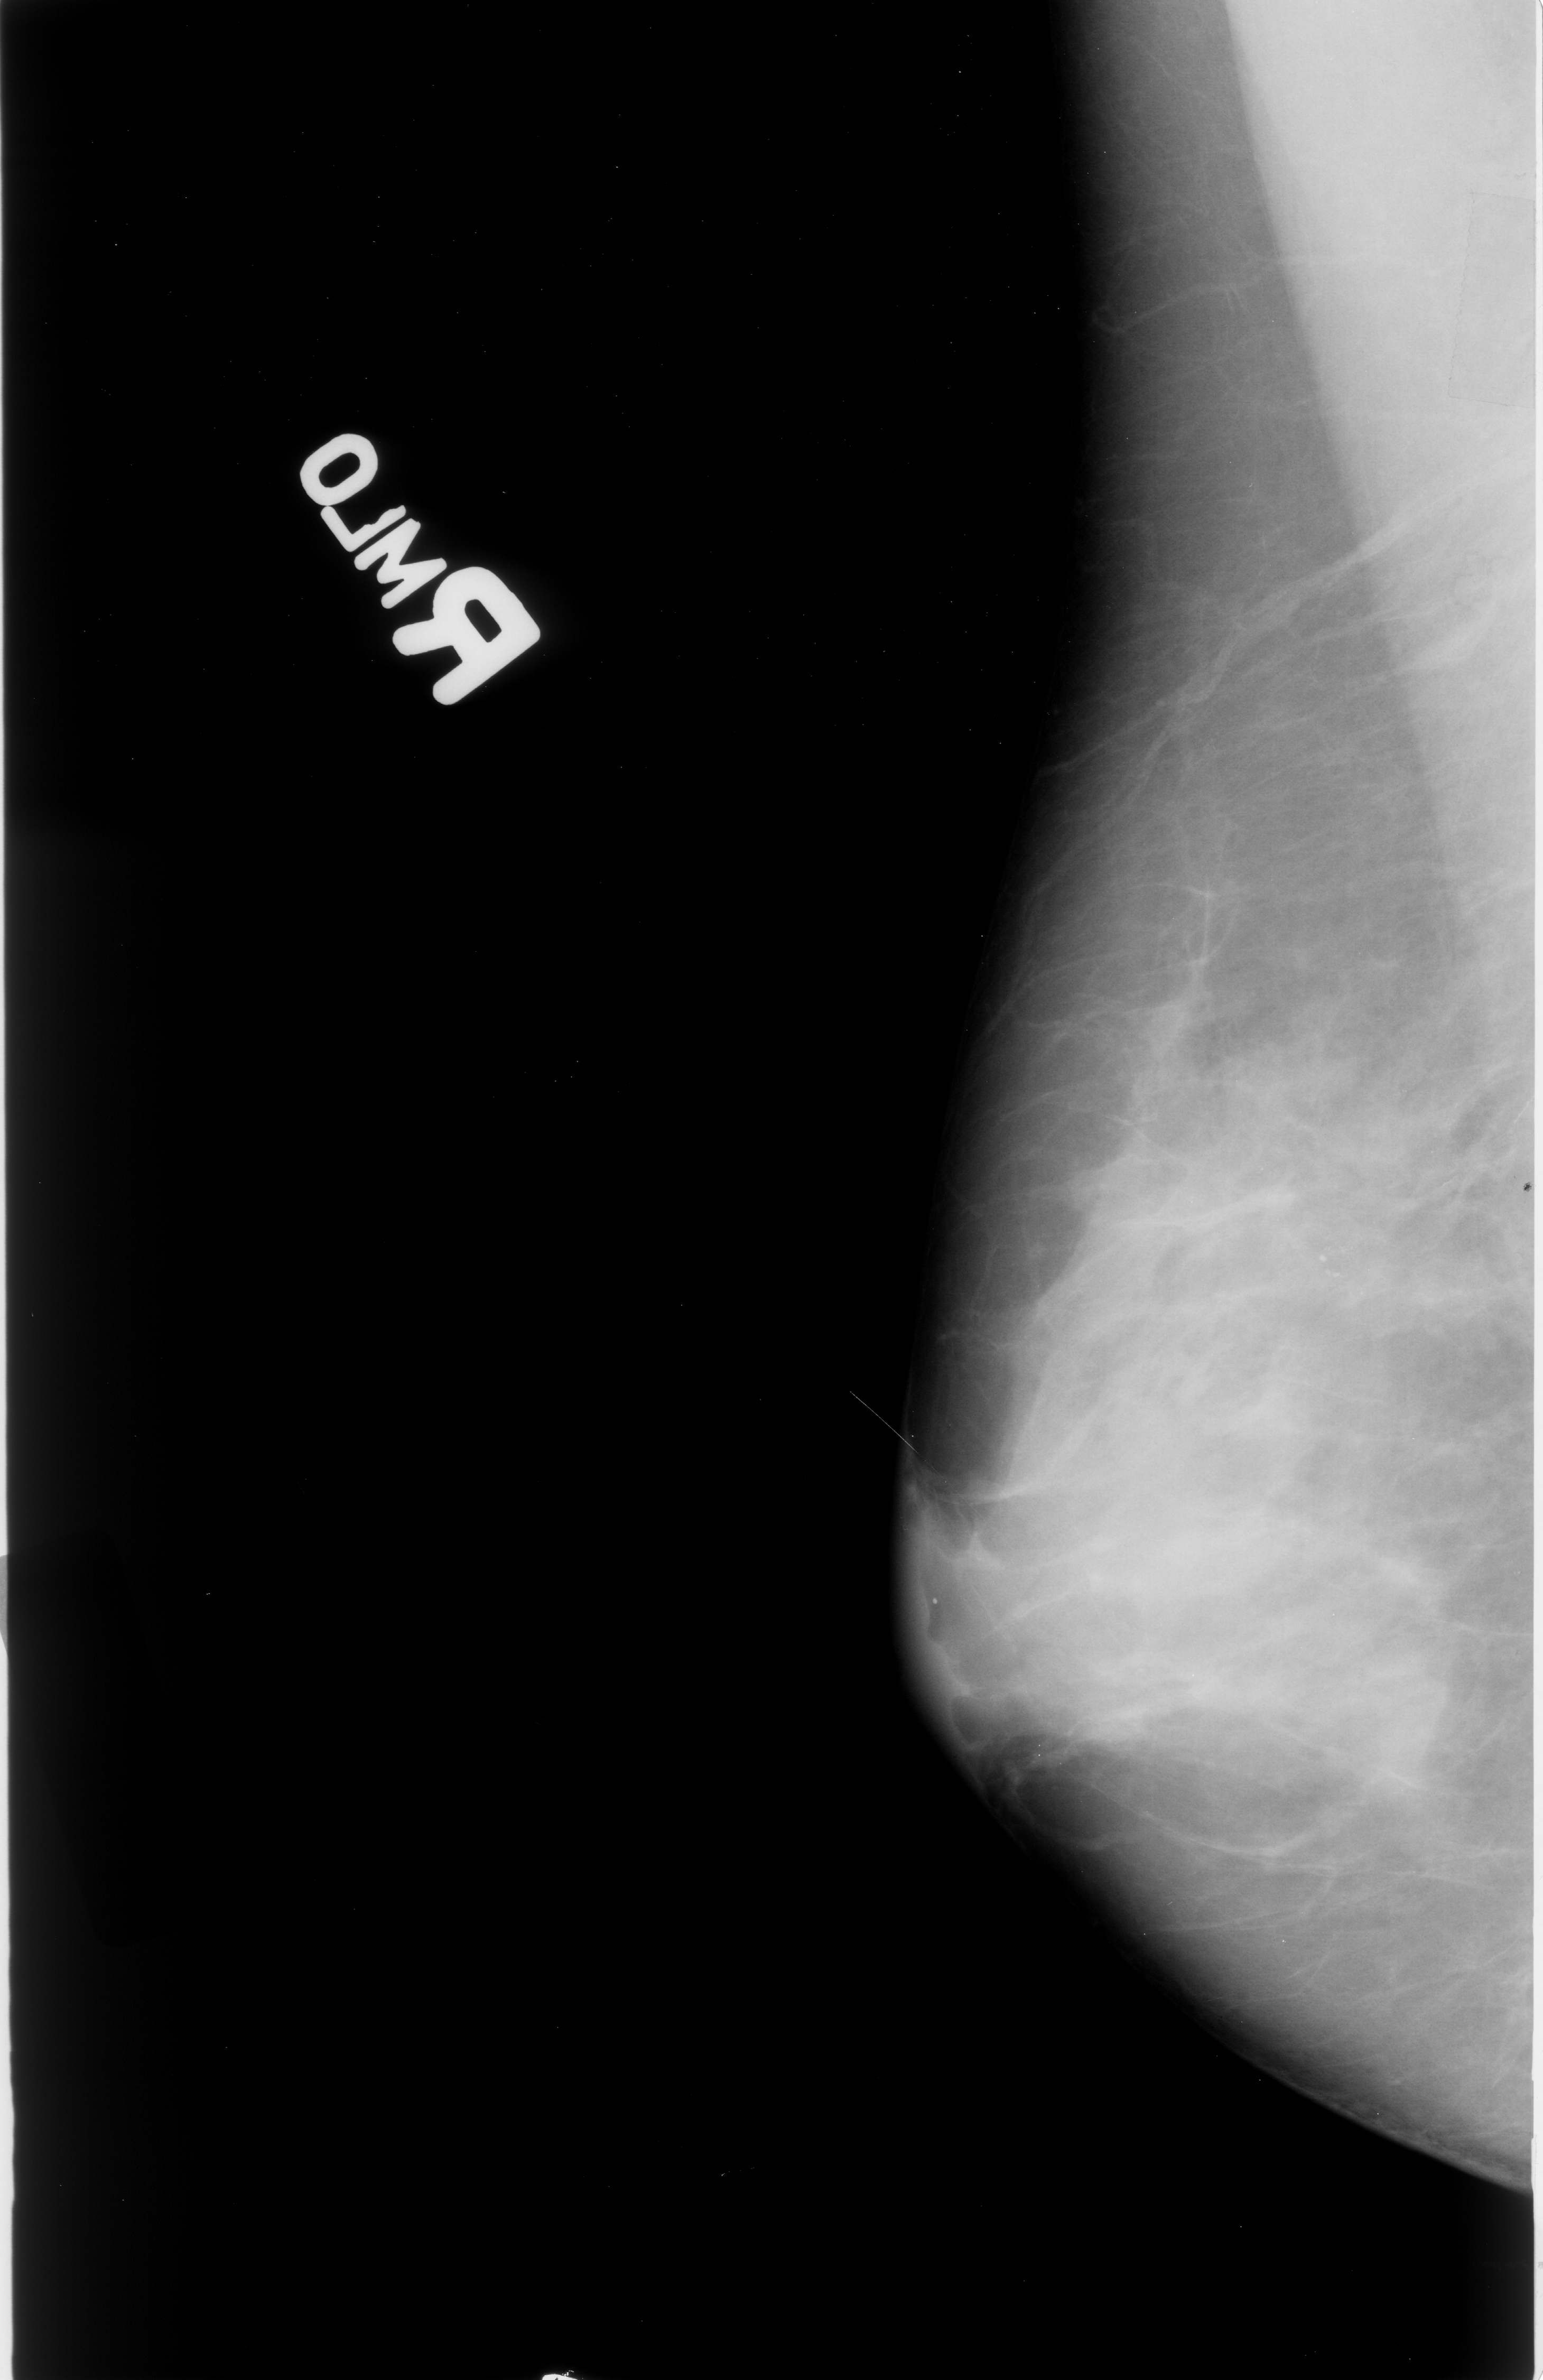
Scanned film-screen mammogram, right breast, mediolateral oblique (MLO) view.
Finding: calcifications, morphology pleomorphic, distribution clustered; BI-RADS assessment category 4; subtlety rating 4 on a 1 (subtle) to 5 (obvious) scale; pathology result (as recorded, not read from the image): malignant.